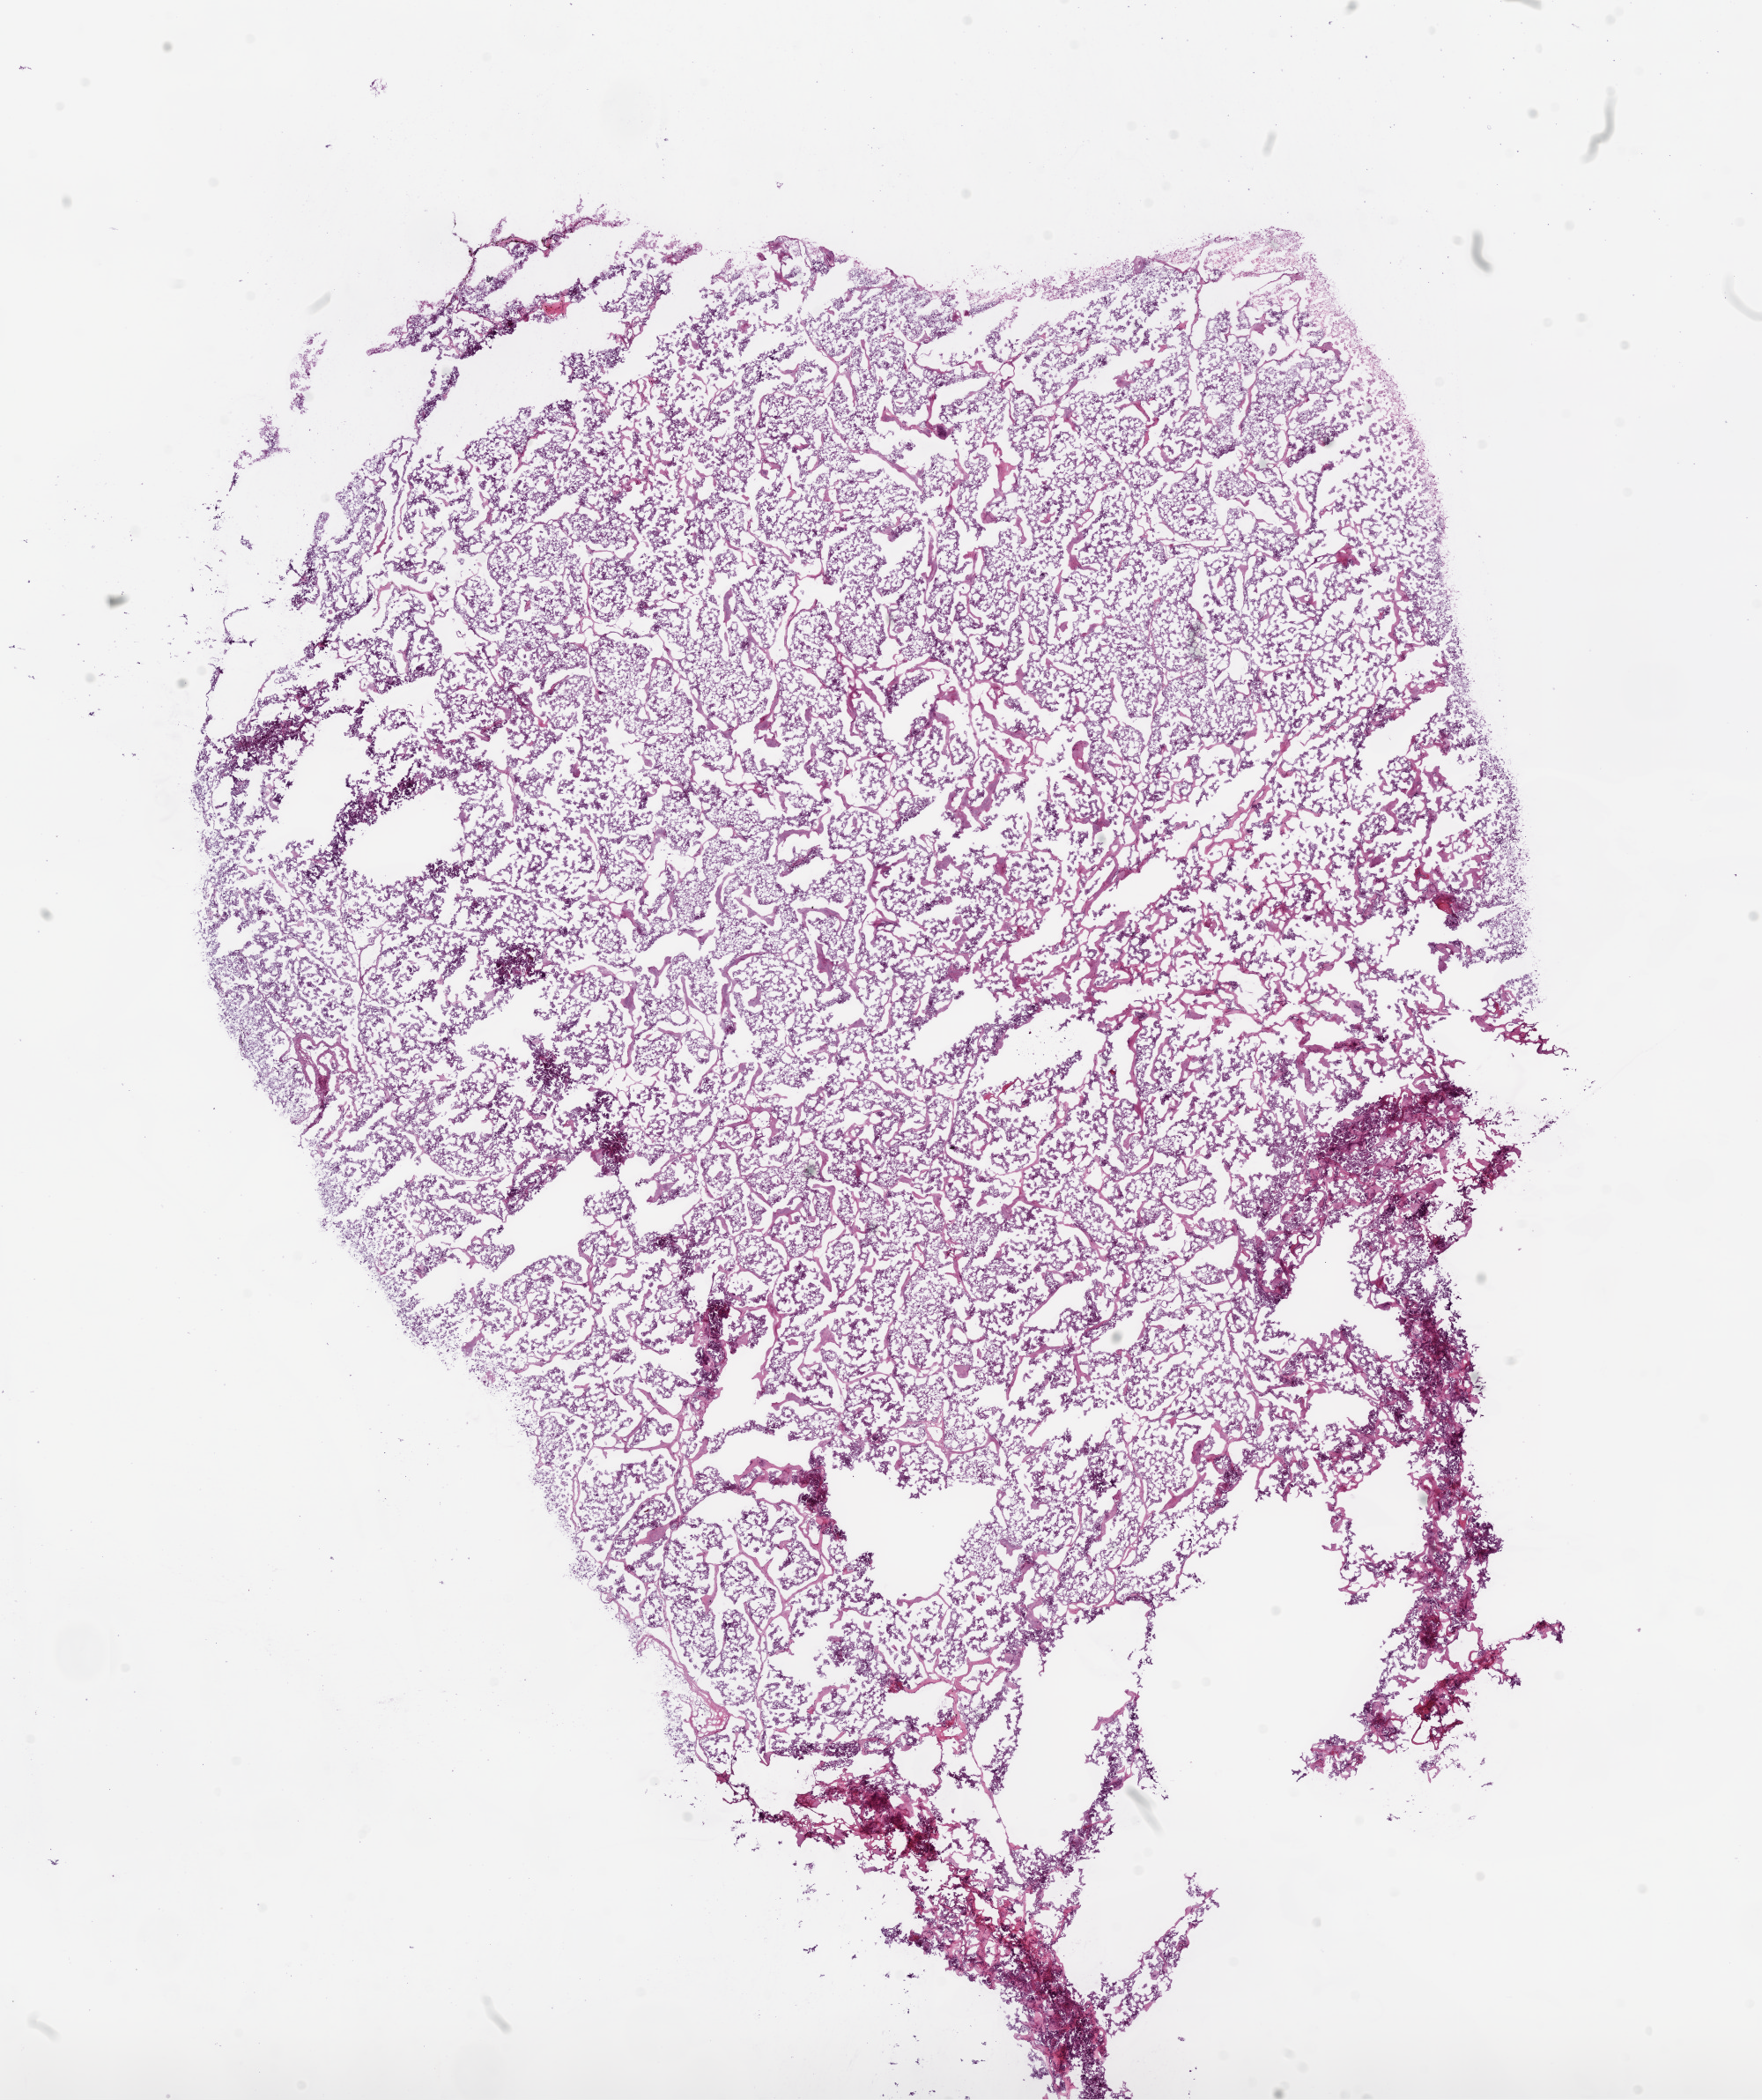
Hematoxylin and eosin (H&E) stained whole-slide image, low-resolution overview of the scanned area, about 16.0 x 19.1 mm (slide scanned at 20x); frozen section; primary tumour sample from the kidney. Patient: male, age at initial diagnosis 56 years. Histologic grade: G3 (poorly differentiated). Pathologist review of this section (percent, as recorded): tumour cells 95%, tumour nuclei 80%, normal cells 0%, stromal cells 5%, necrosis 0%.
• diagnosis: Clear cell adenocarcinoma, NOS
• lymph nodes positive (case pathology): 0 of 1 examined
• AJCC pathologic stage: III